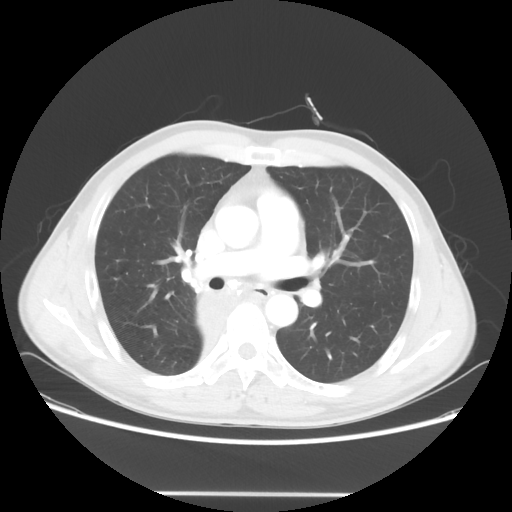
Chest CT, one axial slice; 120 kVp; lung window (W 1500 / L -600 HU); 512 × 512 image matrix. Male patient, age 47 years. Case-level facts recorded for this patient, not image findings: clinical TNM (as recorded): T2 N0 M0; histopathological grade: G2.
Annotated regions visible in this slice (rectangle marked by the reading radiologist):
- lung tumour (recorded histology: squamous cell carcinoma): bounding box (x1, y1, x2, y2) in pixels: (180, 283, 229, 352)